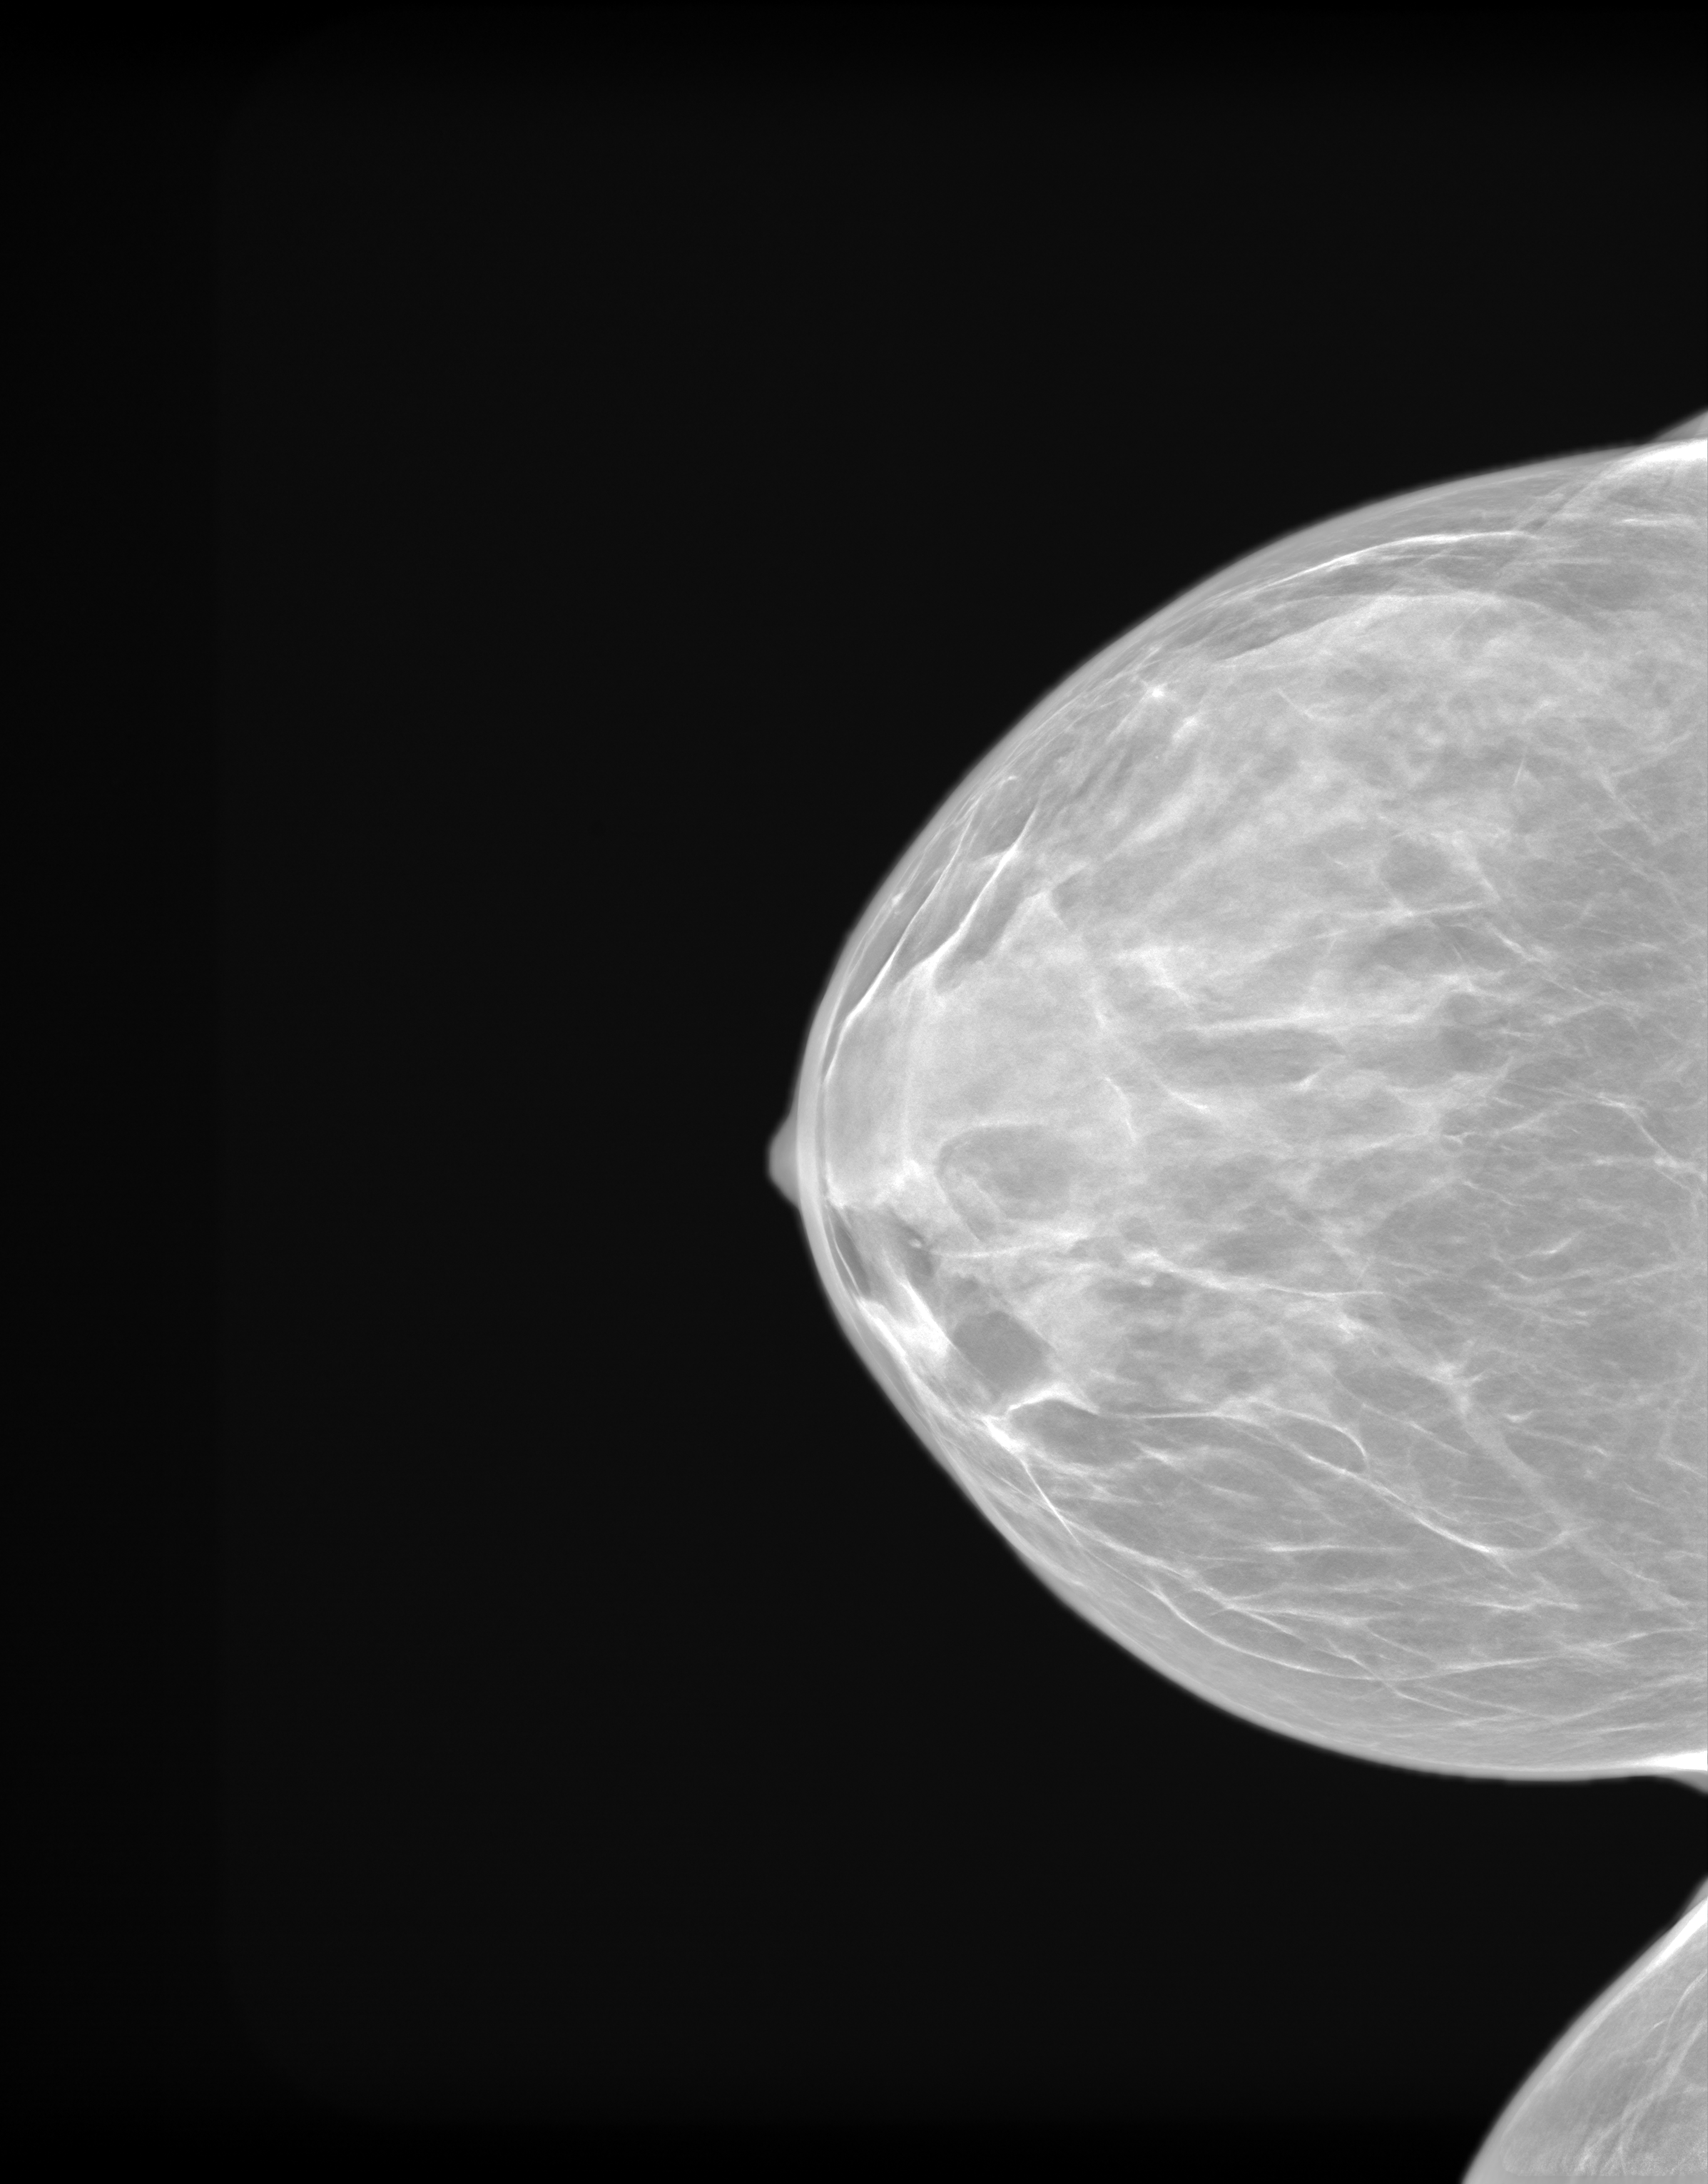
Screening examination, system: SenoIris_1SP2(440). Patient: female, 49 years.
Image type: synthesized 2-D view from tomosynthesis. Breast: right. Projection: CC view.